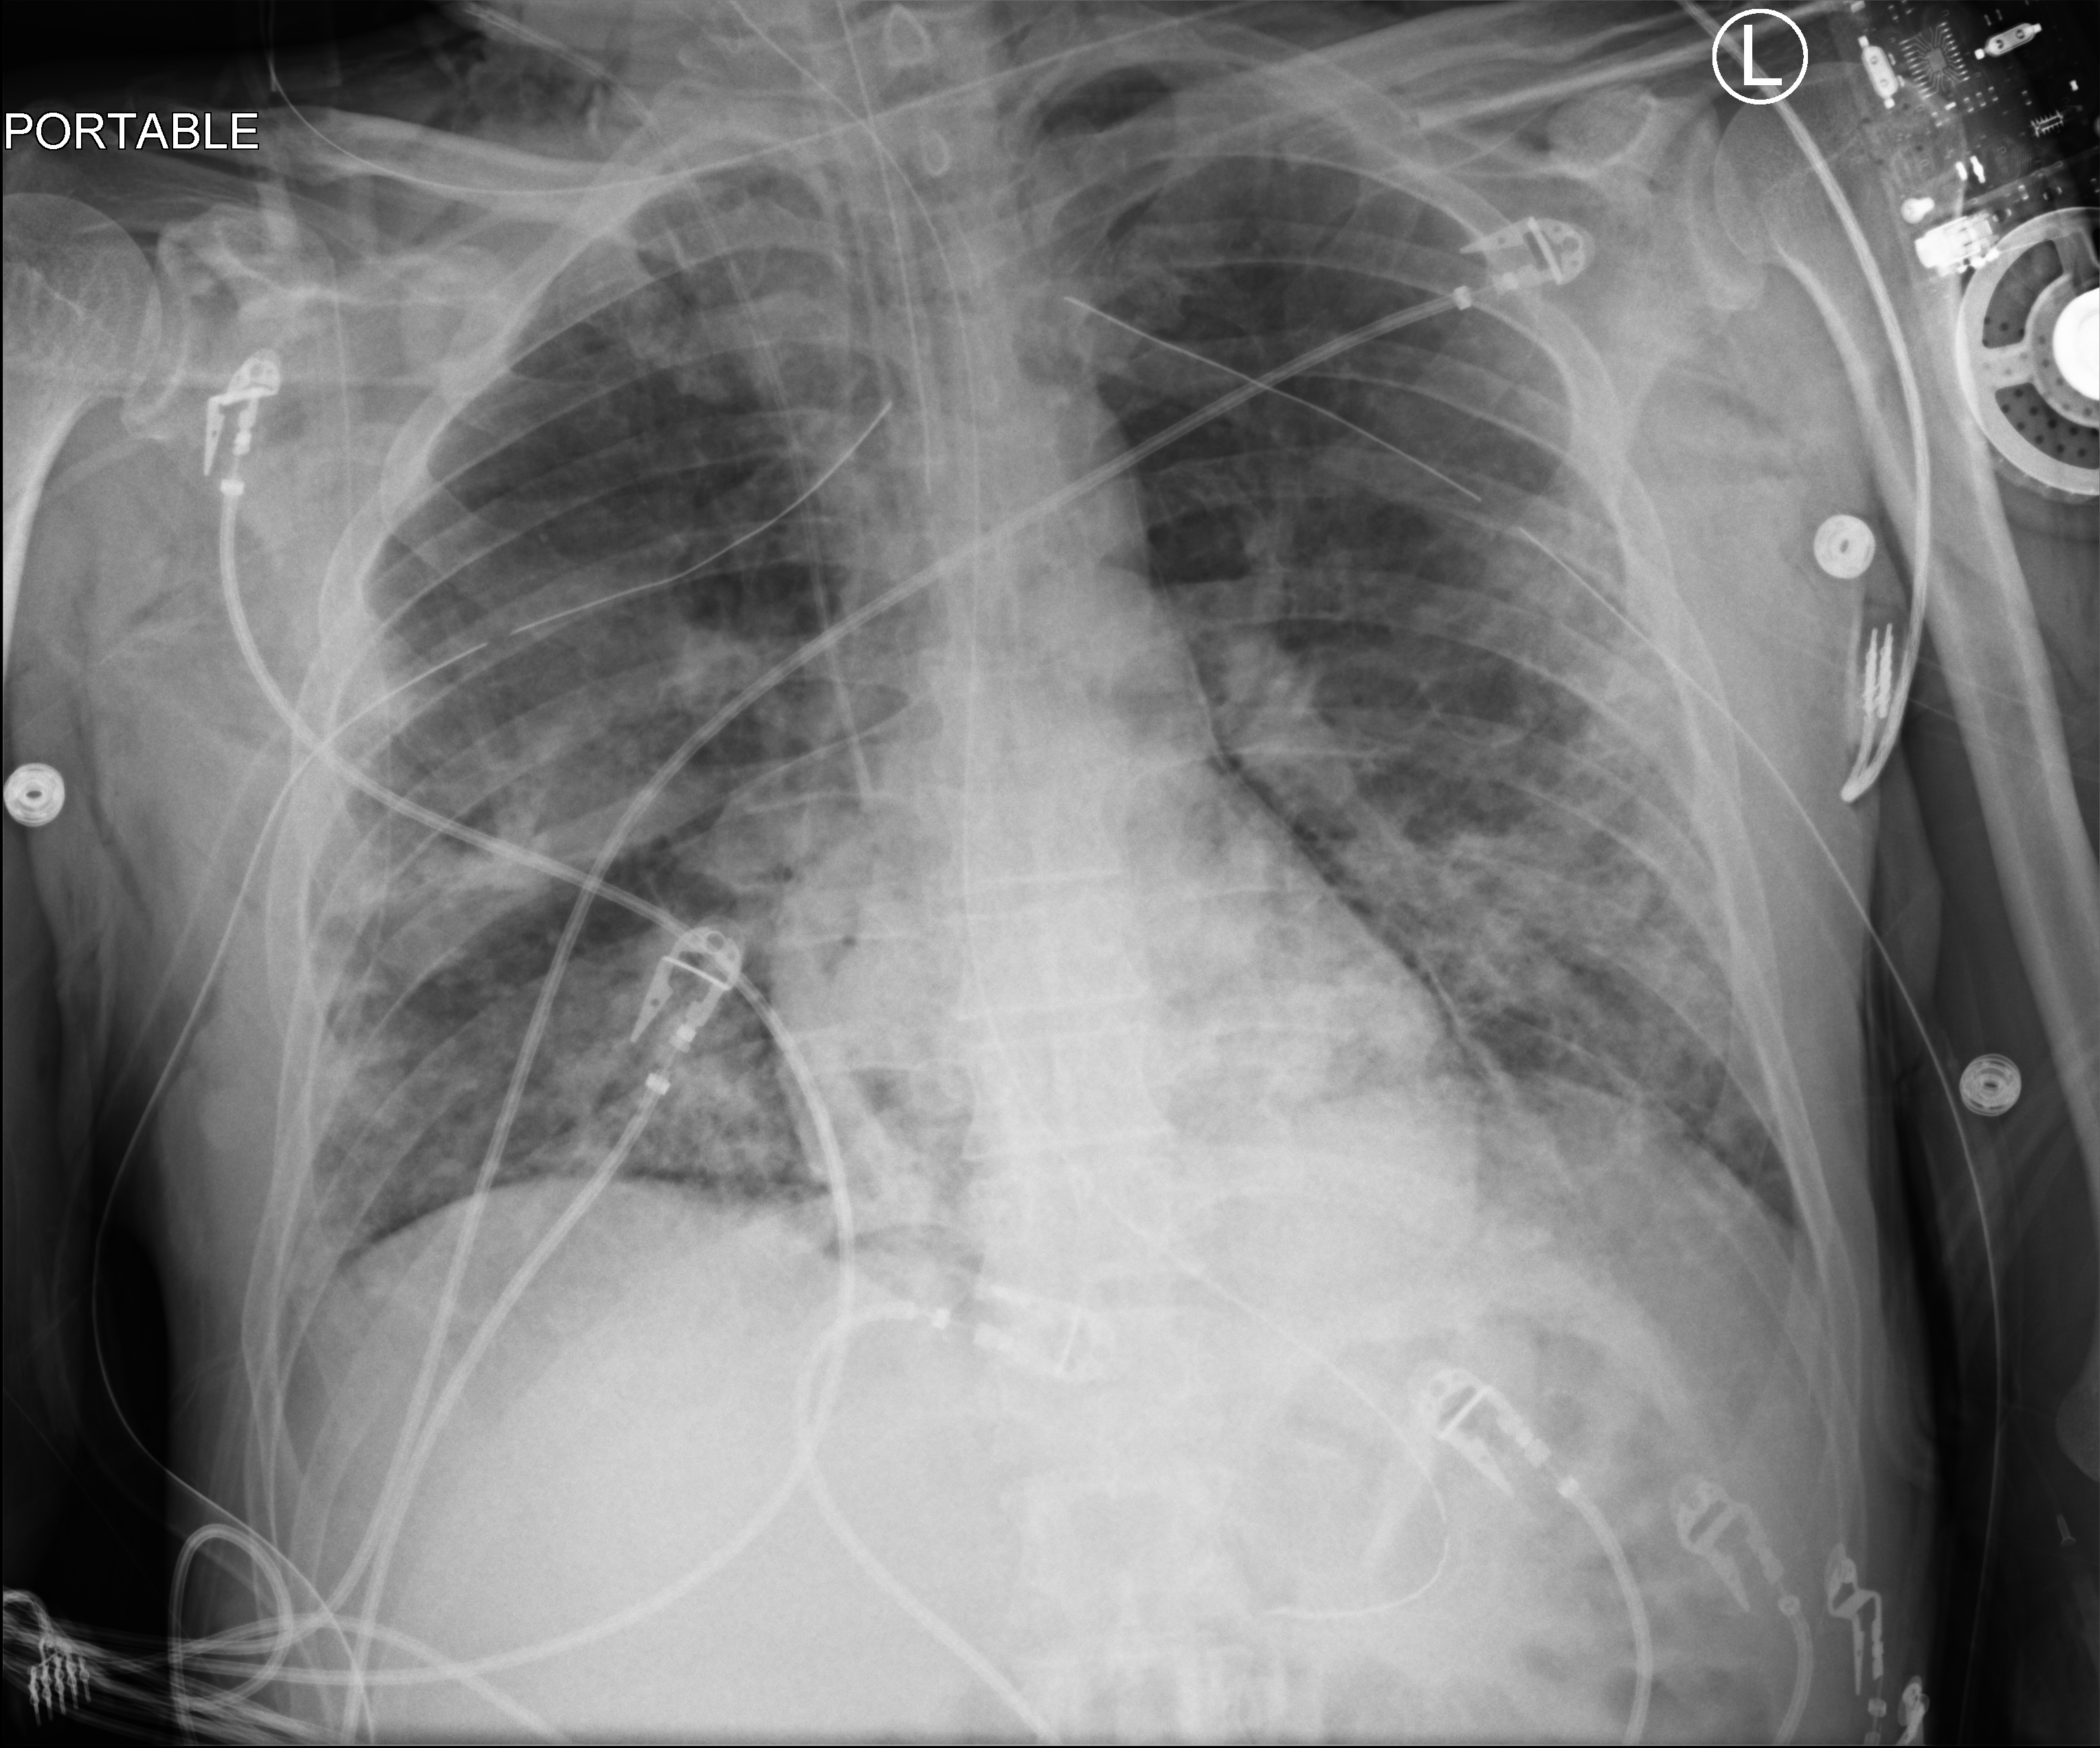
Portable chest radiograph; anteroposterior (AP) projection. Patient hospitalised with COVID-19; male, aged 18–59 years.
Hospital-stay facts (about this admission, not read from this image; timing relative to this image not recorded):
- smoking status (admission record): never